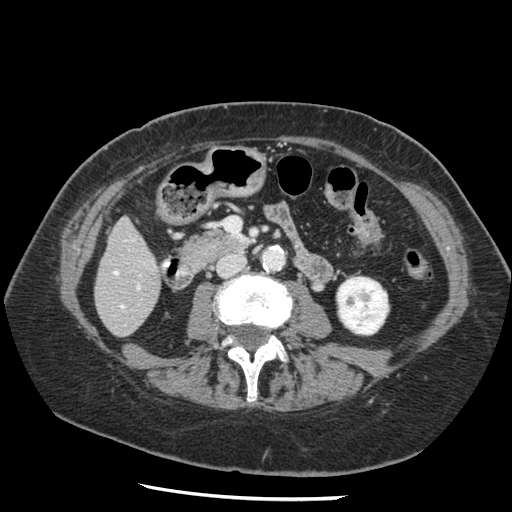
Contrast-enhanced abdominal CT, one axial slice. Slice 37 of 148 in the series (ordered by position). Reconstruction kernel STANDARD. 120 kVp. Intravenous contrast given. Soft-tissue window (W 400 / L 40 HU). 2.5 mm slice thickness. 512 × 512 image matrix, field of view 330 × 330 mm. Female patient, age 85 years. From the clinical record (not read from this slice): diagnosis: colorectal cancer liver metastases, imaged before liver resection; multiple liver metastases: no; largest metastasis: 0.9 cm; disease in both lobes: no.
Outlined on this slice (expert manual segmentation):
- hepatic veins: bounding box (x1, y1, x2, y2) in pixels: (114, 271, 124, 308)
- liver: (96, 220, 161, 336)
- planned liver remnant (the part of the liver to remain after resection): (96, 220, 161, 333)